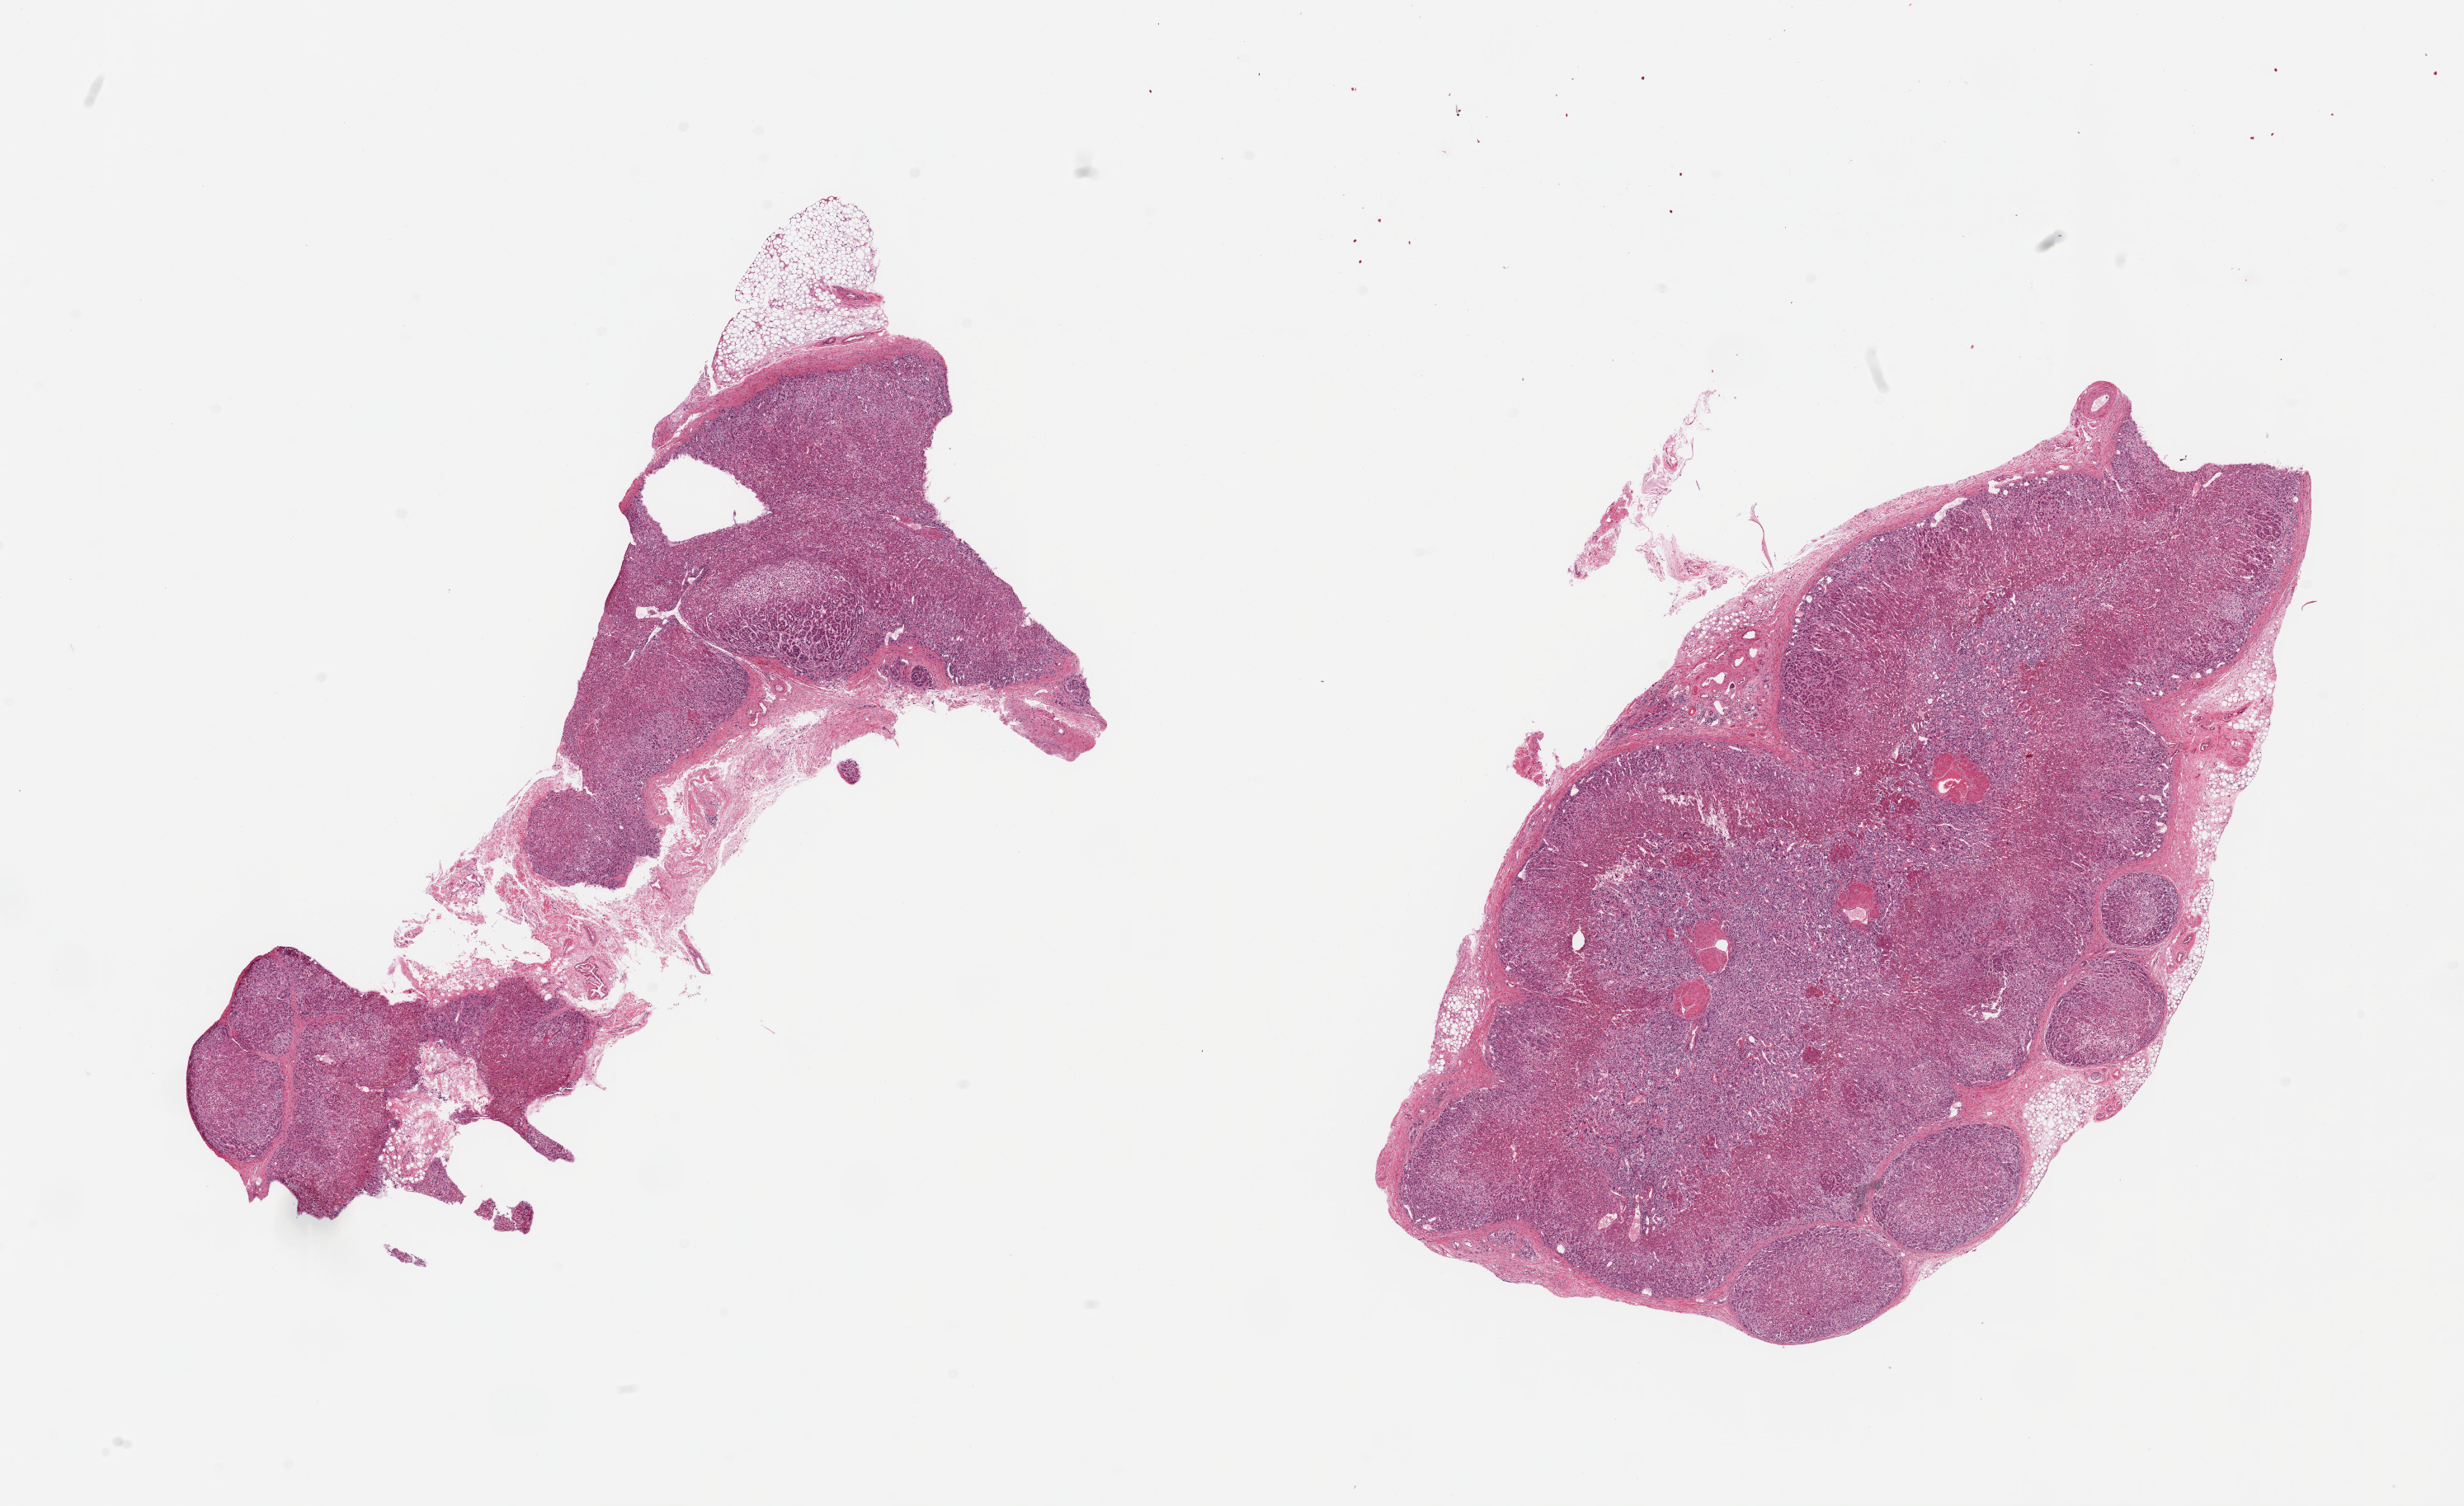
Haematoxylin and eosin whole-slide image, shown as a low-resolution overview of the whole scanned area (about 23.6 x 14.4 mm); PAXgene-fixed paraffin-embedded (PFPE) section; section of adrenal gland (target tissue); donor tissue sample. Donor sex: male.
Pathologist's review note for this sample: 2 pieces, mainly cortex, ~7x2.5mm focus of medulla, well-preserved, valuable specimen; Trace adherent fat.